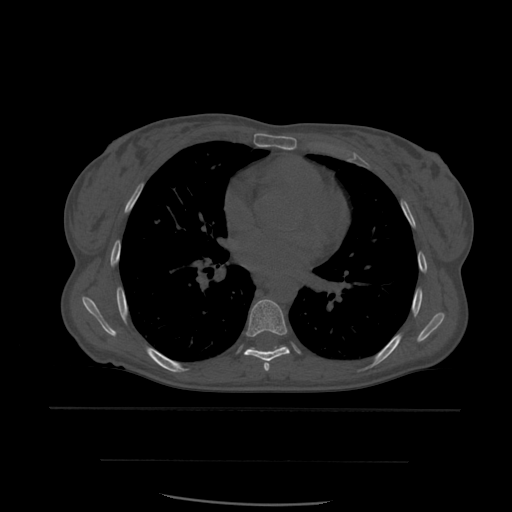
CT including the spine, one axial slice; bone window (W 1800 / L 400 HU); 1.25 mm slice thickness; 512 × 512 image matrix. Patient age 48 years. From the clinical record (not read from this slice): primary cancer: lung.
Annotated regions visible in this slice (semi-automatic segmentation, software-assisted and operator-edited):
- T6 vertebra: bounding box [x1, y1, x2, y2] px = [264, 363, 269, 372]
- T7 vertebra: [244, 299, 290, 370]
- T8 vertebra: [249, 346, 286, 351]